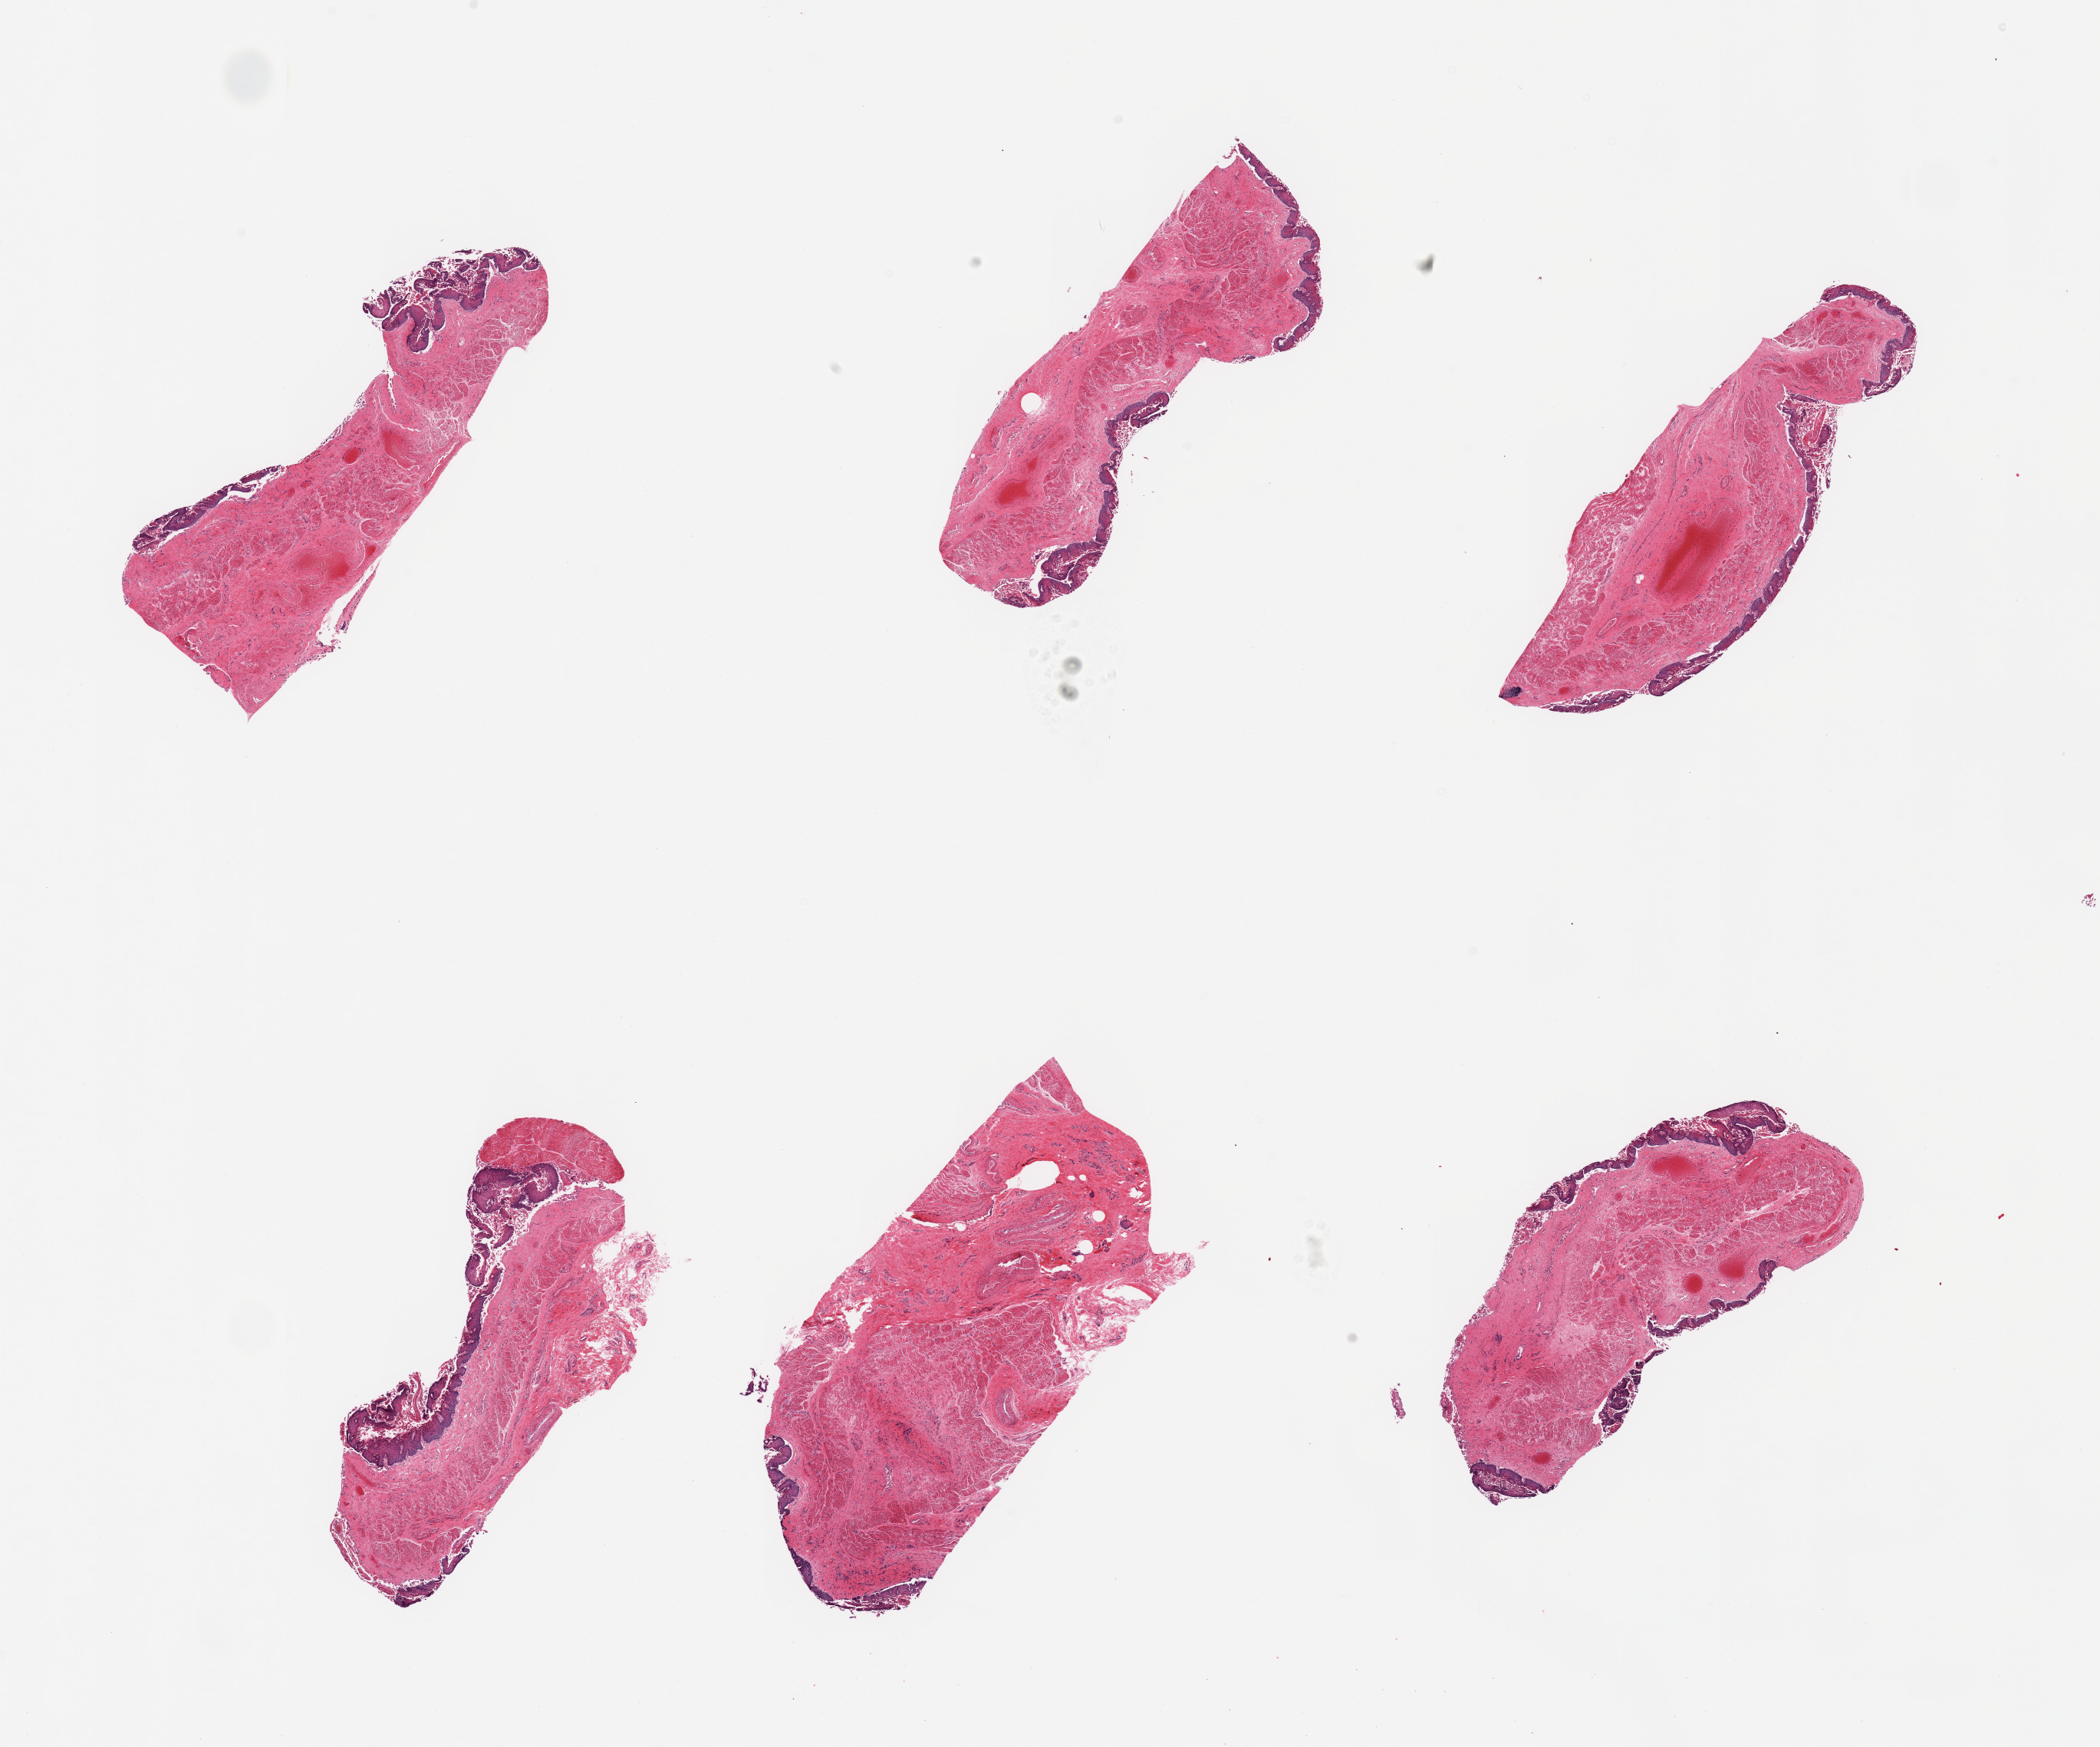
Whole-slide image, H&E stain, brightfield — a low-resolution overview of the entire scanned area, about 21.7 x 18.0 mm; PAXgene-fixed, paraffin-embedded tissue; section of esophageal mucous membrane (target tissue); donor tissue sample. Male donor.
Review note (as recorded): 6 pieces, squamous mucosa sloughing, residual thickness up to ~0.15m.